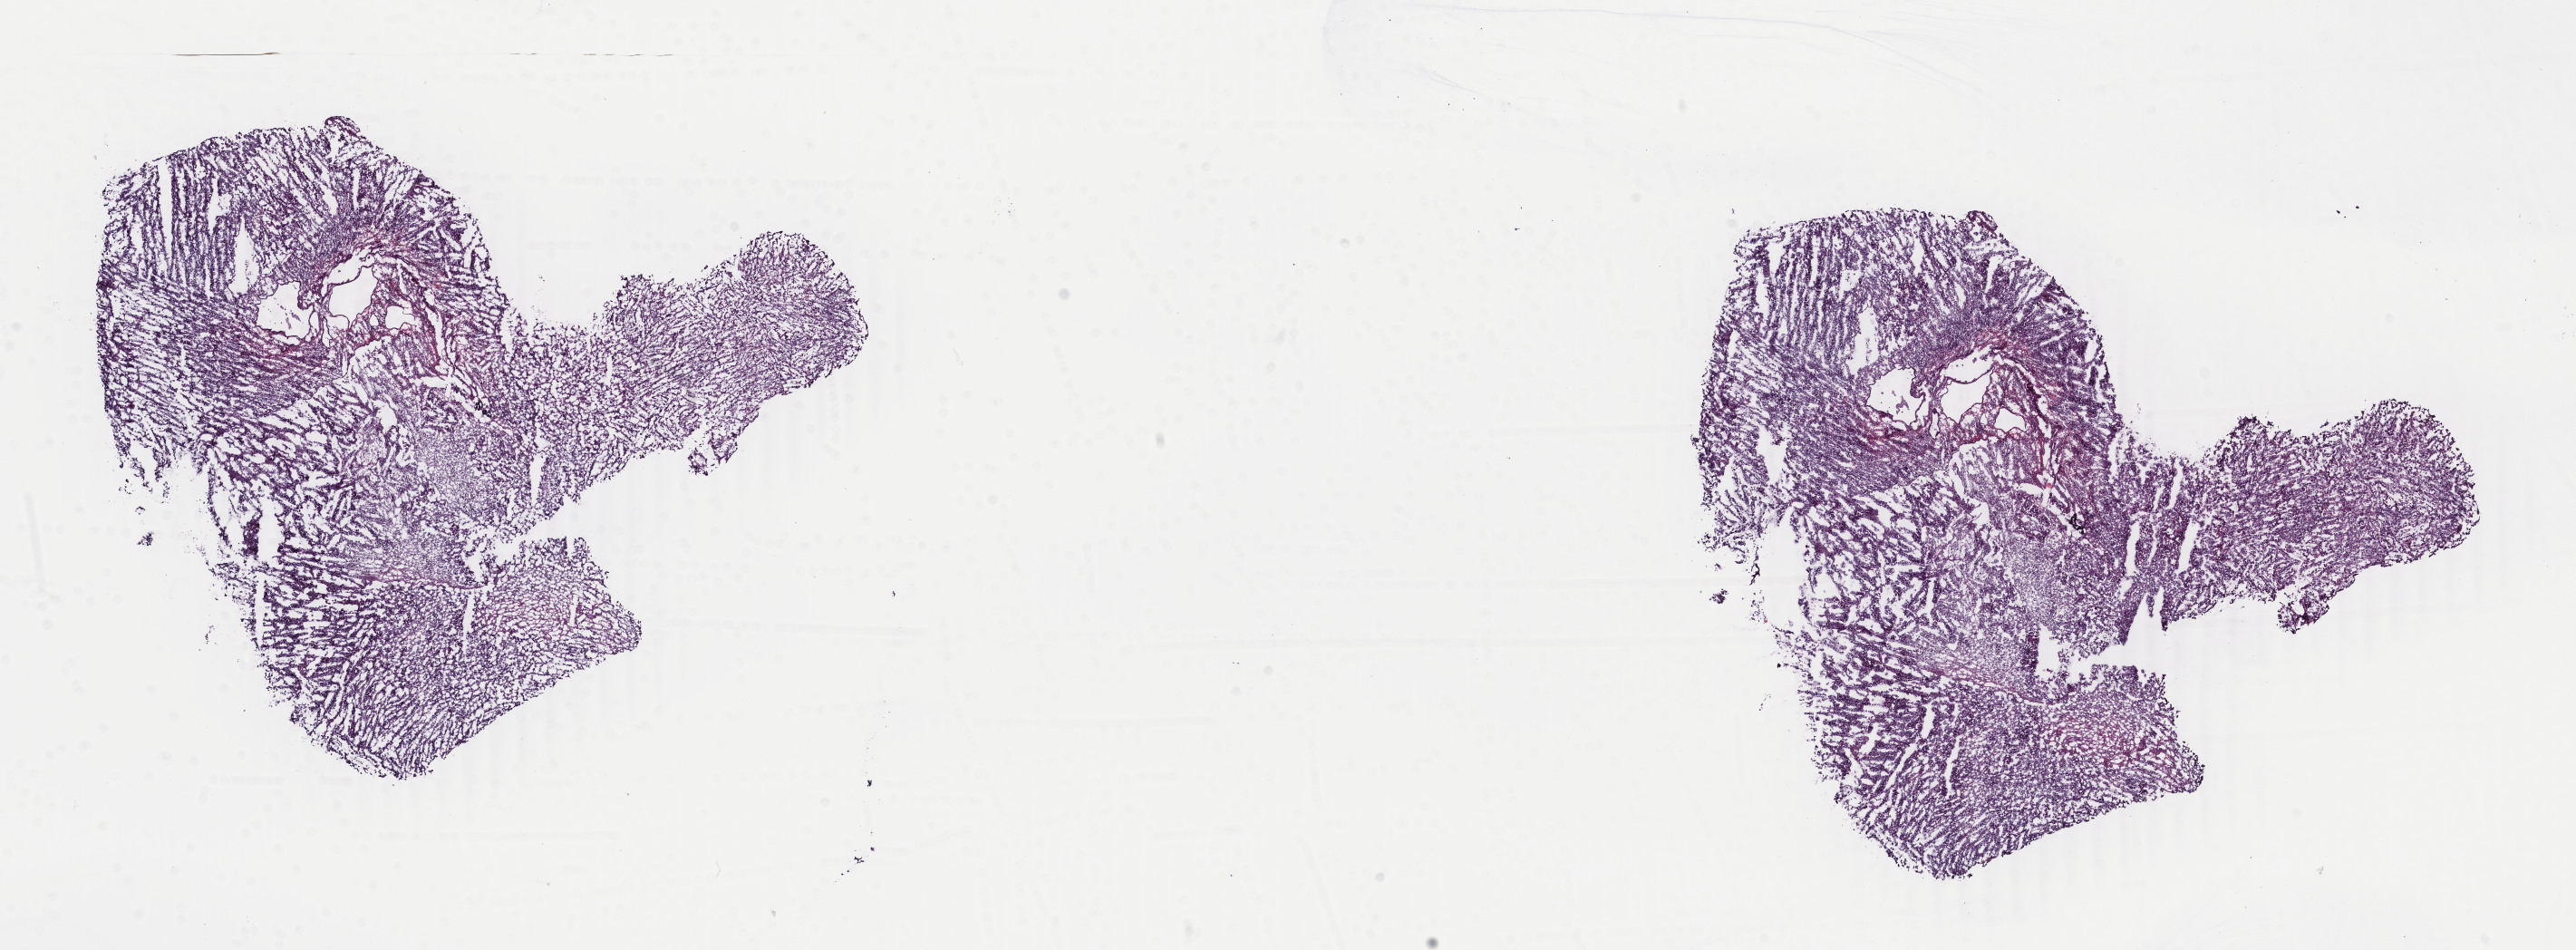
H&E whole-slide image, a low-resolution overview of the entire scanned area, about 22.6 x 8.3 mm (acquisition: 40x scan); frozen section from the top of the tissue portion; primary tumour sample from the uterus. Female patient; age at initial diagnosis 65 years. Pathologist review of this section (percent, as recorded): tumour cells 80%, tumour nuclei 80%, normal cells 10%, stromal cells 5%, necrosis 5%. Inflammatory infiltration, as recorded: lymphocyte infiltration 70%, monocyte infiltration 10%, neutrophil infiltration 5%.
Diagnosis: Mullerian mixed tumor. FIGO stage: IA.